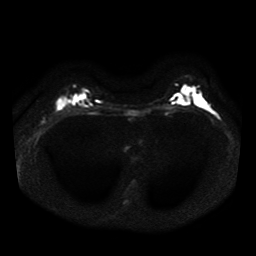
Breast MRI, one axial slice; slice 28 of 41 in the series (ordered by position); diffusion-weighted series; image 2 of 4 stored at this slice position (different b-values; order by instance number); 1.5 T; 256 × 256 image matrix, field of view 330 × 330 mm. Female patient.
Annotated regions visible in this slice (outlined manually by an expert reader):
- tumour on diffusion-weighted imaging: box from (x=58, y=98) to (x=64, y=106) px